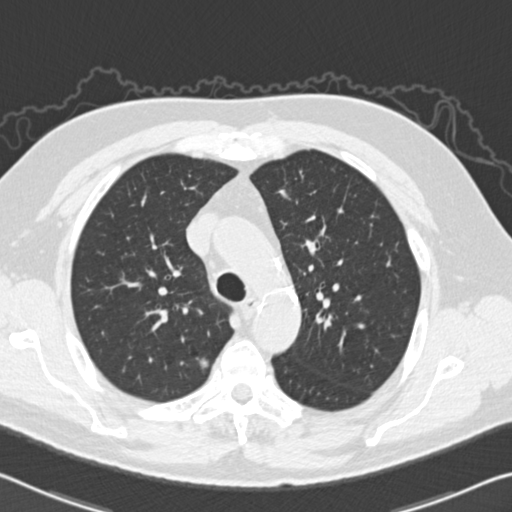
Low-dose screening chest CT, axial slice. Baseline annual screen. Lung window (W 1500 / L -600 HU). Standard (soft-tissue) reconstruction kernel (B30f). Slice 40 of 151 in the series. Male participant, aged 64 years at enrolment. Former smoker at enrolment.
- Expert reader's lesion annotation, bounding box [x1, y1, x2, y2] px = [185, 340, 229, 388].
- Screening reader's record for this exam (one nodule recorded; not confirmed to be the boxed lesion): non-calcified nodule or mass ≥4 mm, right upper lobe, 10 × 8 mm, spiculated (stellate) margins, soft tissue attenuation.
- Participant outcome: lung cancer diagnosed 99 days after this screen — adenocarcinoma, NOS, right upper lobe, poorly differentiated (G3), stage IA (AJCC 6th edition), 11 mm at pathology.